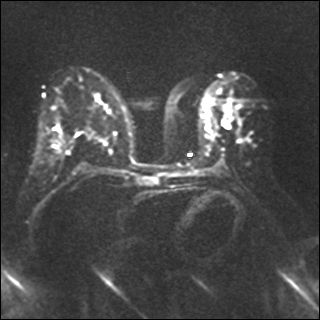
Breast MRI, one axial slice; slice 18 of 35 in the series (ordered by position); diffusion-weighted series; image 2 of 4 stored at this slice position (different b-values; order by instance number); 1.5 T; 320 × 320 image matrix. Female patient.
Annotated regions visible in this slice (outlined manually by an expert reader):
- tumour on diffusion-weighted imaging: bounding box <224,121,228,127> (left, top, right, bottom; pixels)